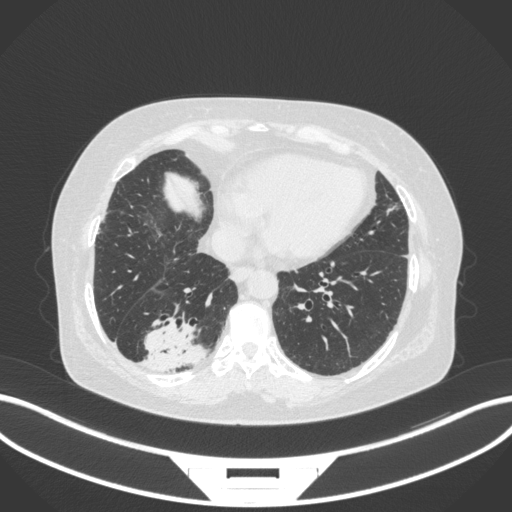
Chest CT, one axial slice; slice 69 of 303 in the series (ordered by position); reconstruction kernel B31f; 120 kVp; lung window (W 1500 / L -600 HU); 1 mm slice thickness; 512 × 512 image matrix. Patient: female, 65 years. From the clinical record (not read from this slice): clinical TNM (as recorded): T2b N1 M0; histopathological grade: G1.
Outlined on this slice (bounding box drawn by a radiologist):
- lung tumour (recorded histology: adenocarcinoma): box from (x=134, y=315) to (x=212, y=373) px